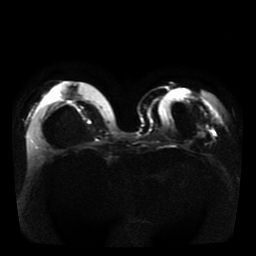
Breast MRI, one axial slice; slice 14 of 41 in the series (ordered by position); diffusion-weighted series; image 2 of 4 stored at this slice position (different b-values; order by instance number); 1.5 T; 256 × 256 image matrix. Female patient.
Structures marked on this image (expert manual segmentation):
- tumour on diffusion-weighted imaging: bounding box [x1, y1, x2, y2] px = [199, 126, 203, 130]